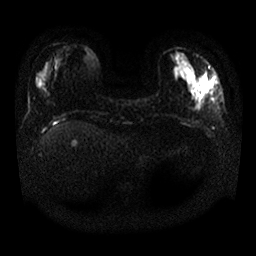
Breast MRI, one axial slice. Slice 6 of 25 in the series (ordered by position). Diffusion-weighted series; image 2 of 4 stored at this slice position (different b-values; order by instance number). 1.5 T. 4 mm slice thickness. 256 × 256 image matrix, field of view 340 × 340 mm. Female patient.
Structures marked on this image (expert manual segmentation):
- tumour on diffusion-weighted imaging: bounding box (x1, y1, x2, y2) in pixels: (200, 70, 209, 88)